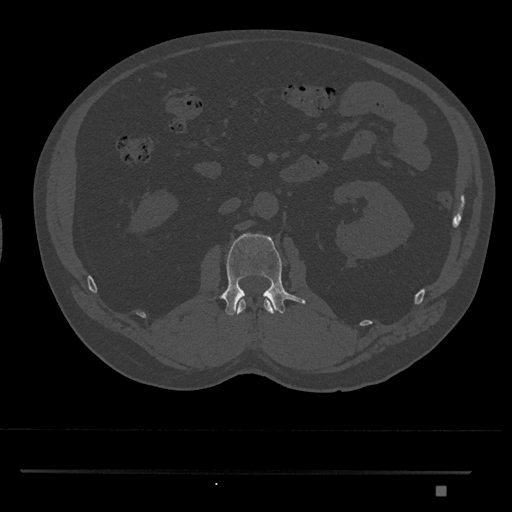
CT including the spine, one axial slice. Slice 769 of 1134 in the series (ordered by position). Reconstruction kernel Br40s/3. 120 kVp. Bone window (W 1800 / L 400 HU). 512 × 512 image matrix, field of view 429 × 429 mm. Patient: male, 65 years. From the clinical record (not read from this slice): primary cancer: prostate.
Structures marked on this image (semi-automatic segmentation, software-assisted and operator-edited):
- L1 vertebra: box from (x=236, y=299) to (x=275, y=315) px
- L2 vertebra: (x=215, y=233)–(x=306, y=316)